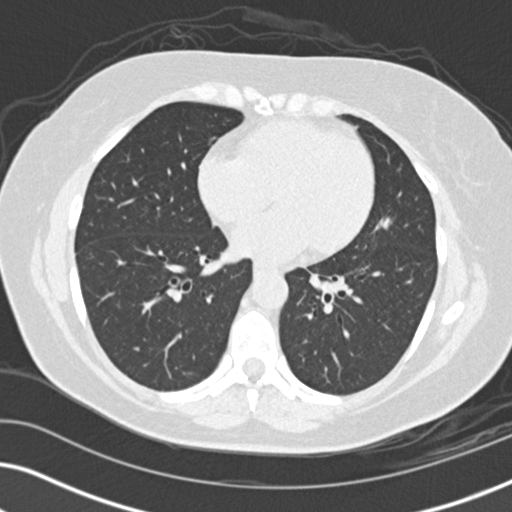
Low-dose screening chest CT, one axial slice; position 70 of 152 along the scan axis; reconstruction kernel B30f; 120 kVp; lung window (W 1500 / L -600 HU); 512 × 512 image matrix, field of view 330 × 330 mm.
Structures marked on this image (manually delineated by an expert):
- lesion 1 (tumor, upper lobe of left lung): bounding box (x1, y1, x2, y2) in pixels: (380, 218, 390, 228)